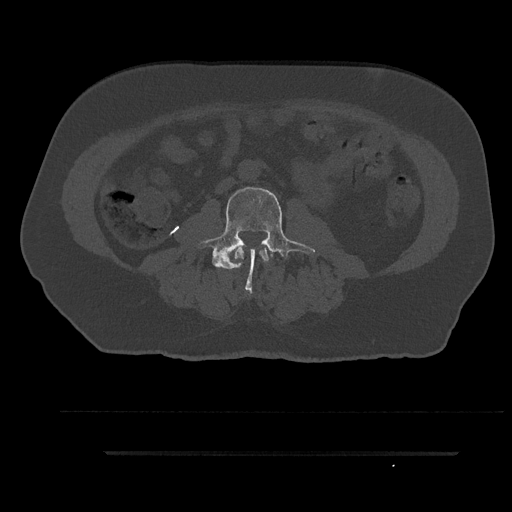
CT including the spine, one axial slice; slice 48 of 797 in the series (ordered by position); reconstruction kernel Br40s/3; 120 kVp; bone window (W 1800 / L 400 HU); 512 × 512 image matrix, field of view 432 × 432 mm. Patient: male, 63 years. Case-level facts recorded for this patient, not image findings: primary cancer: renal; vertebrae with lytic lesions (as recorded): T8.
Structures marked on this image (semi-automatically segmented with operator editing):
- L2 vertebra: bounding box [x1, y1, x2, y2] px = [234, 247, 269, 268]
- L3 vertebra: [197, 185, 315, 292]